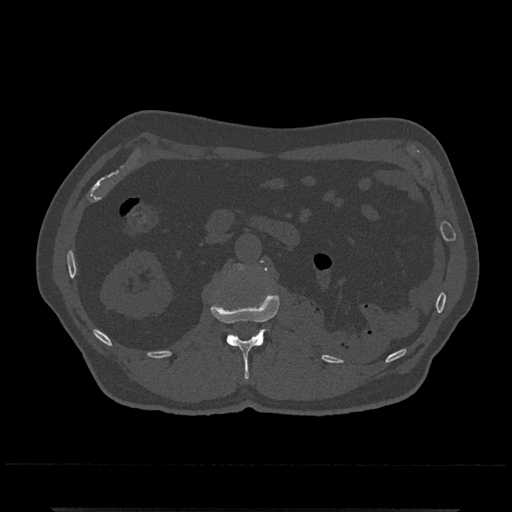
CT including the spine, one axial slice. Position 344 of 797 along the scan axis. Reconstruction kernel Br40s/3. Bone window (W 1800 / L 400 HU). 0.5 mm slice thickness. 512 × 512 image matrix. Male patient, age 67 years. Case-level facts recorded for this patient, not image findings: primary cancer: prostate.
Structures marked on this image (semi-automatic segmentation, software-assisted and operator-edited):
- L1 vertebra: bounding box <211,267,280,380> (left, top, right, bottom; pixels)
- L2 vertebra: <236,260,263,270>